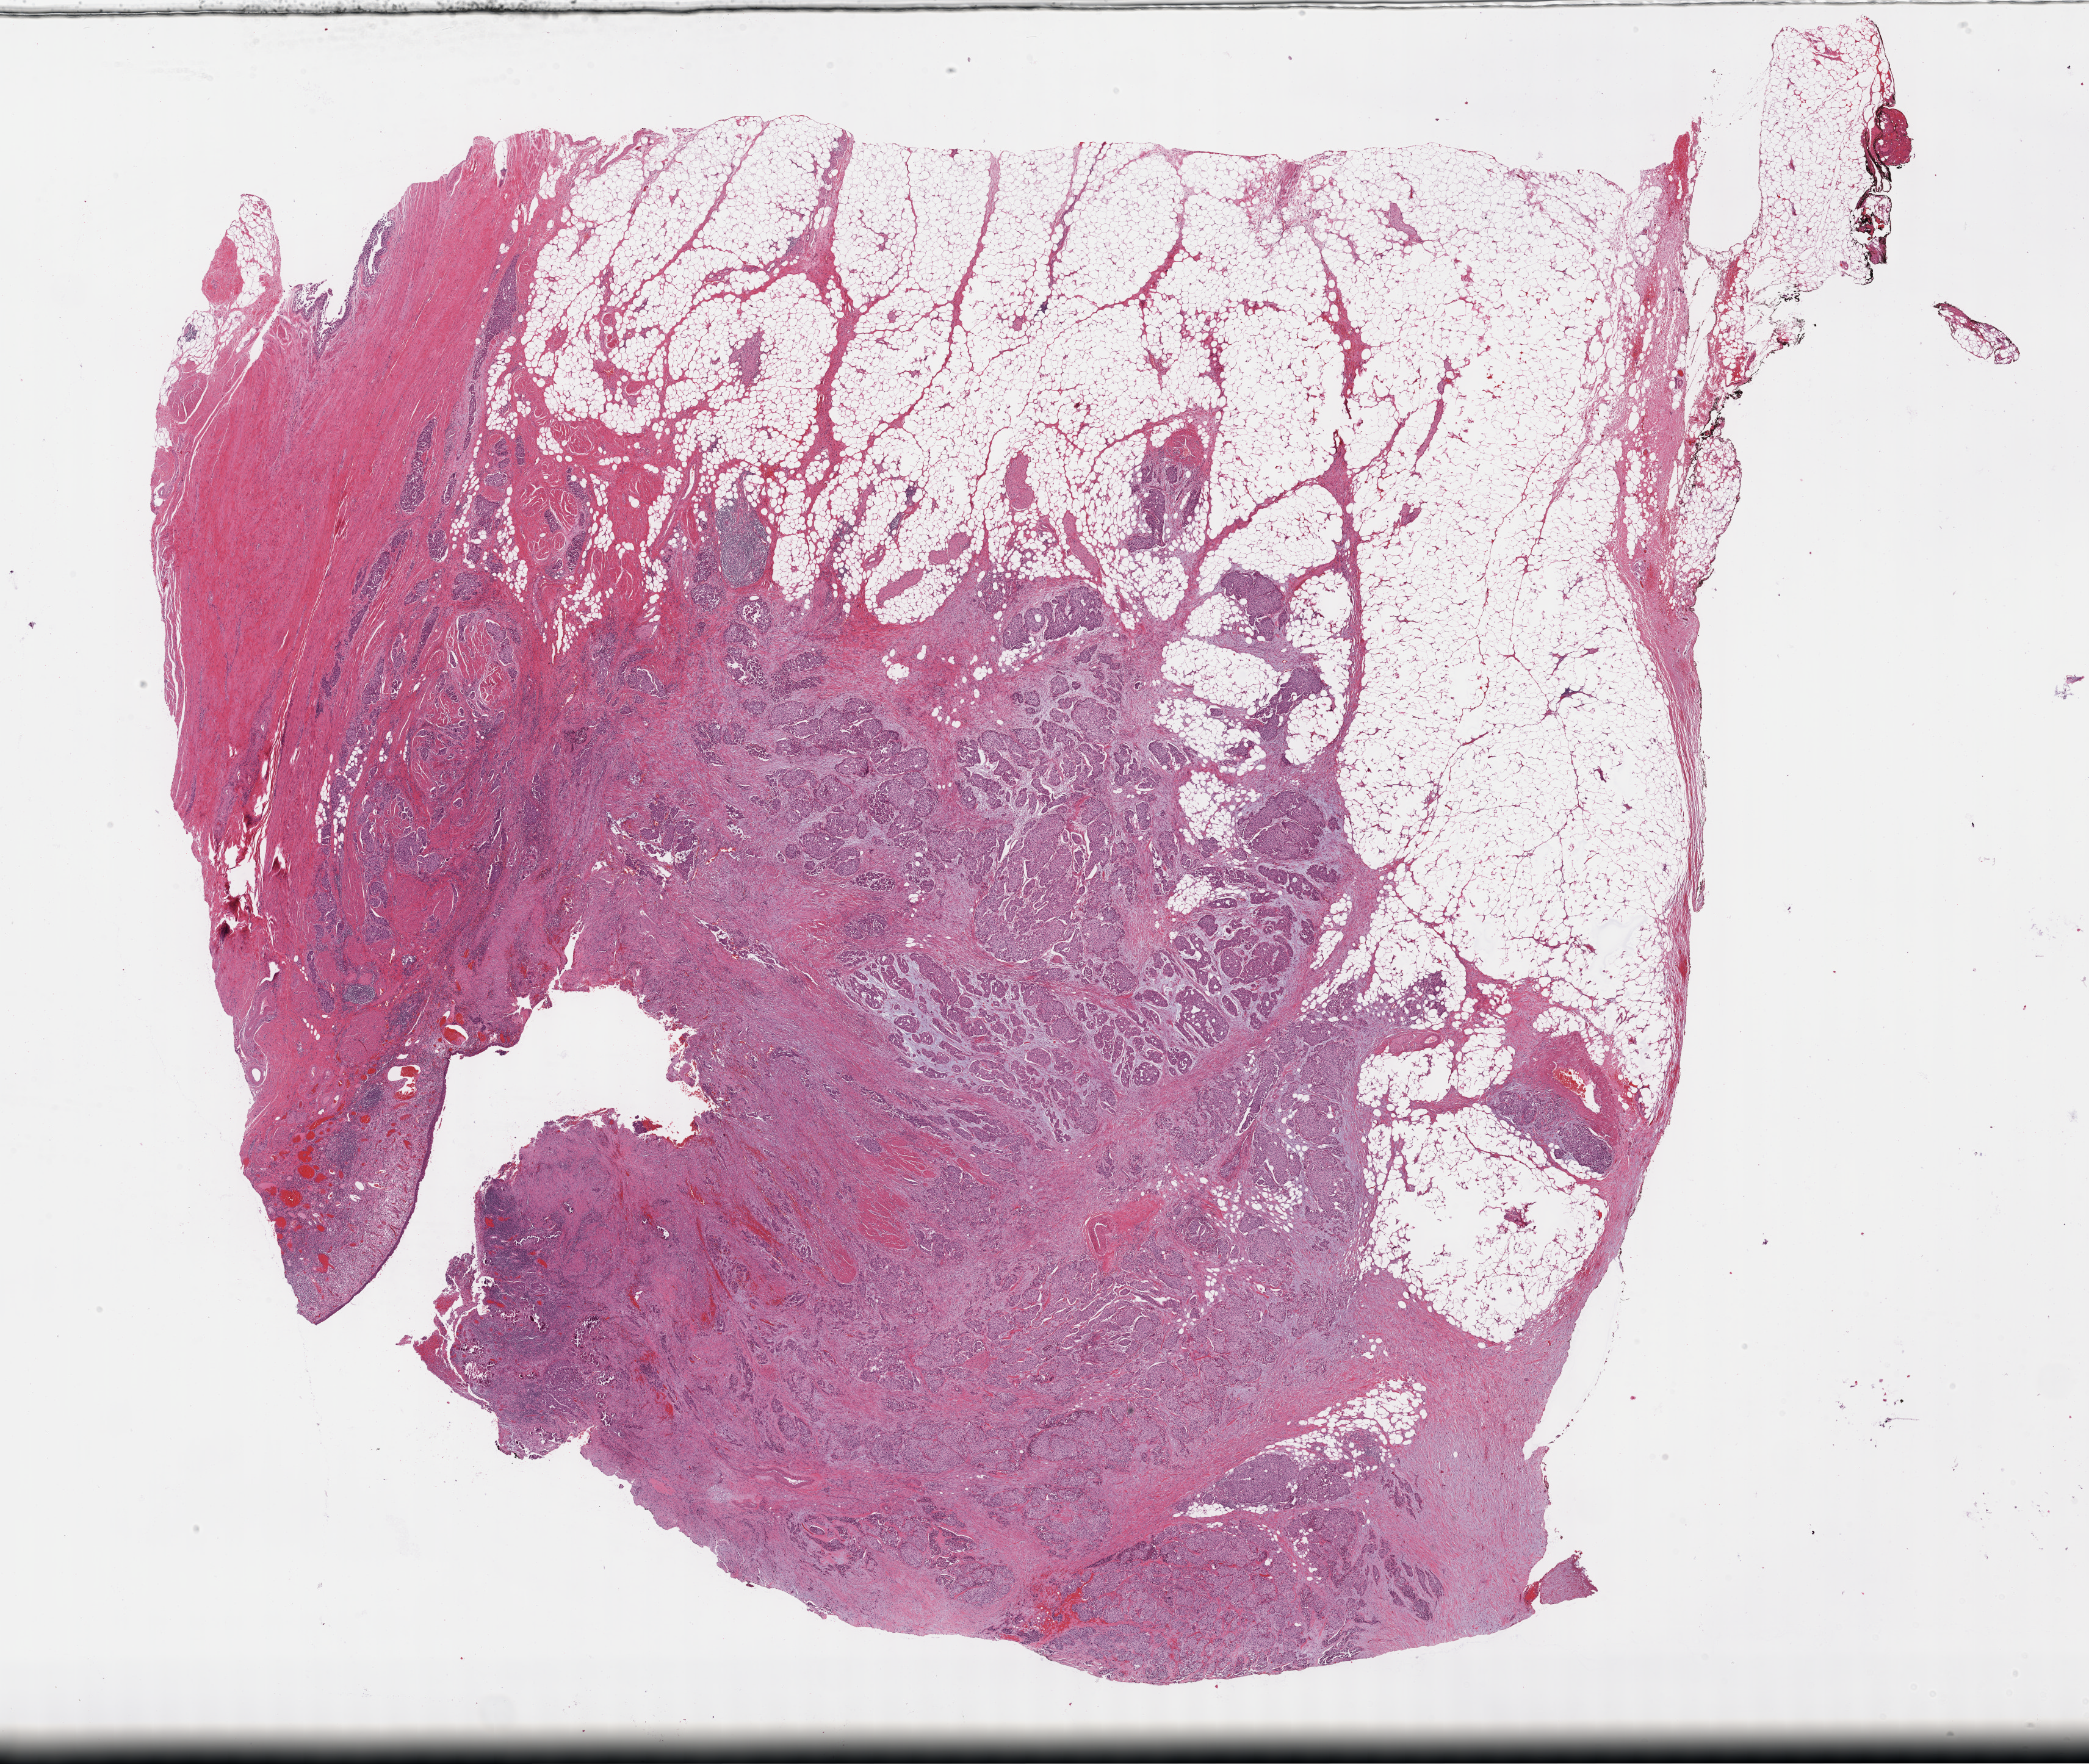
Digitized H&E tissue section (whole slide) — whole scanned area (about 27.7 x 23.4 mm, acquisition: 40x scan) shown as a low-resolution overview; formalin-fixed paraffin-embedded (FFPE) diagnostic section; primary tumour sample from the bladder. Male, age 70 years at initial diagnosis. Histologic grade: high grade.
Lymph nodes positive (case pathology): 7 of 34 examined. AJCC pathologic stage: IV. Pathologic diagnosis: Transitional cell carcinoma (lateral wall of bladder).